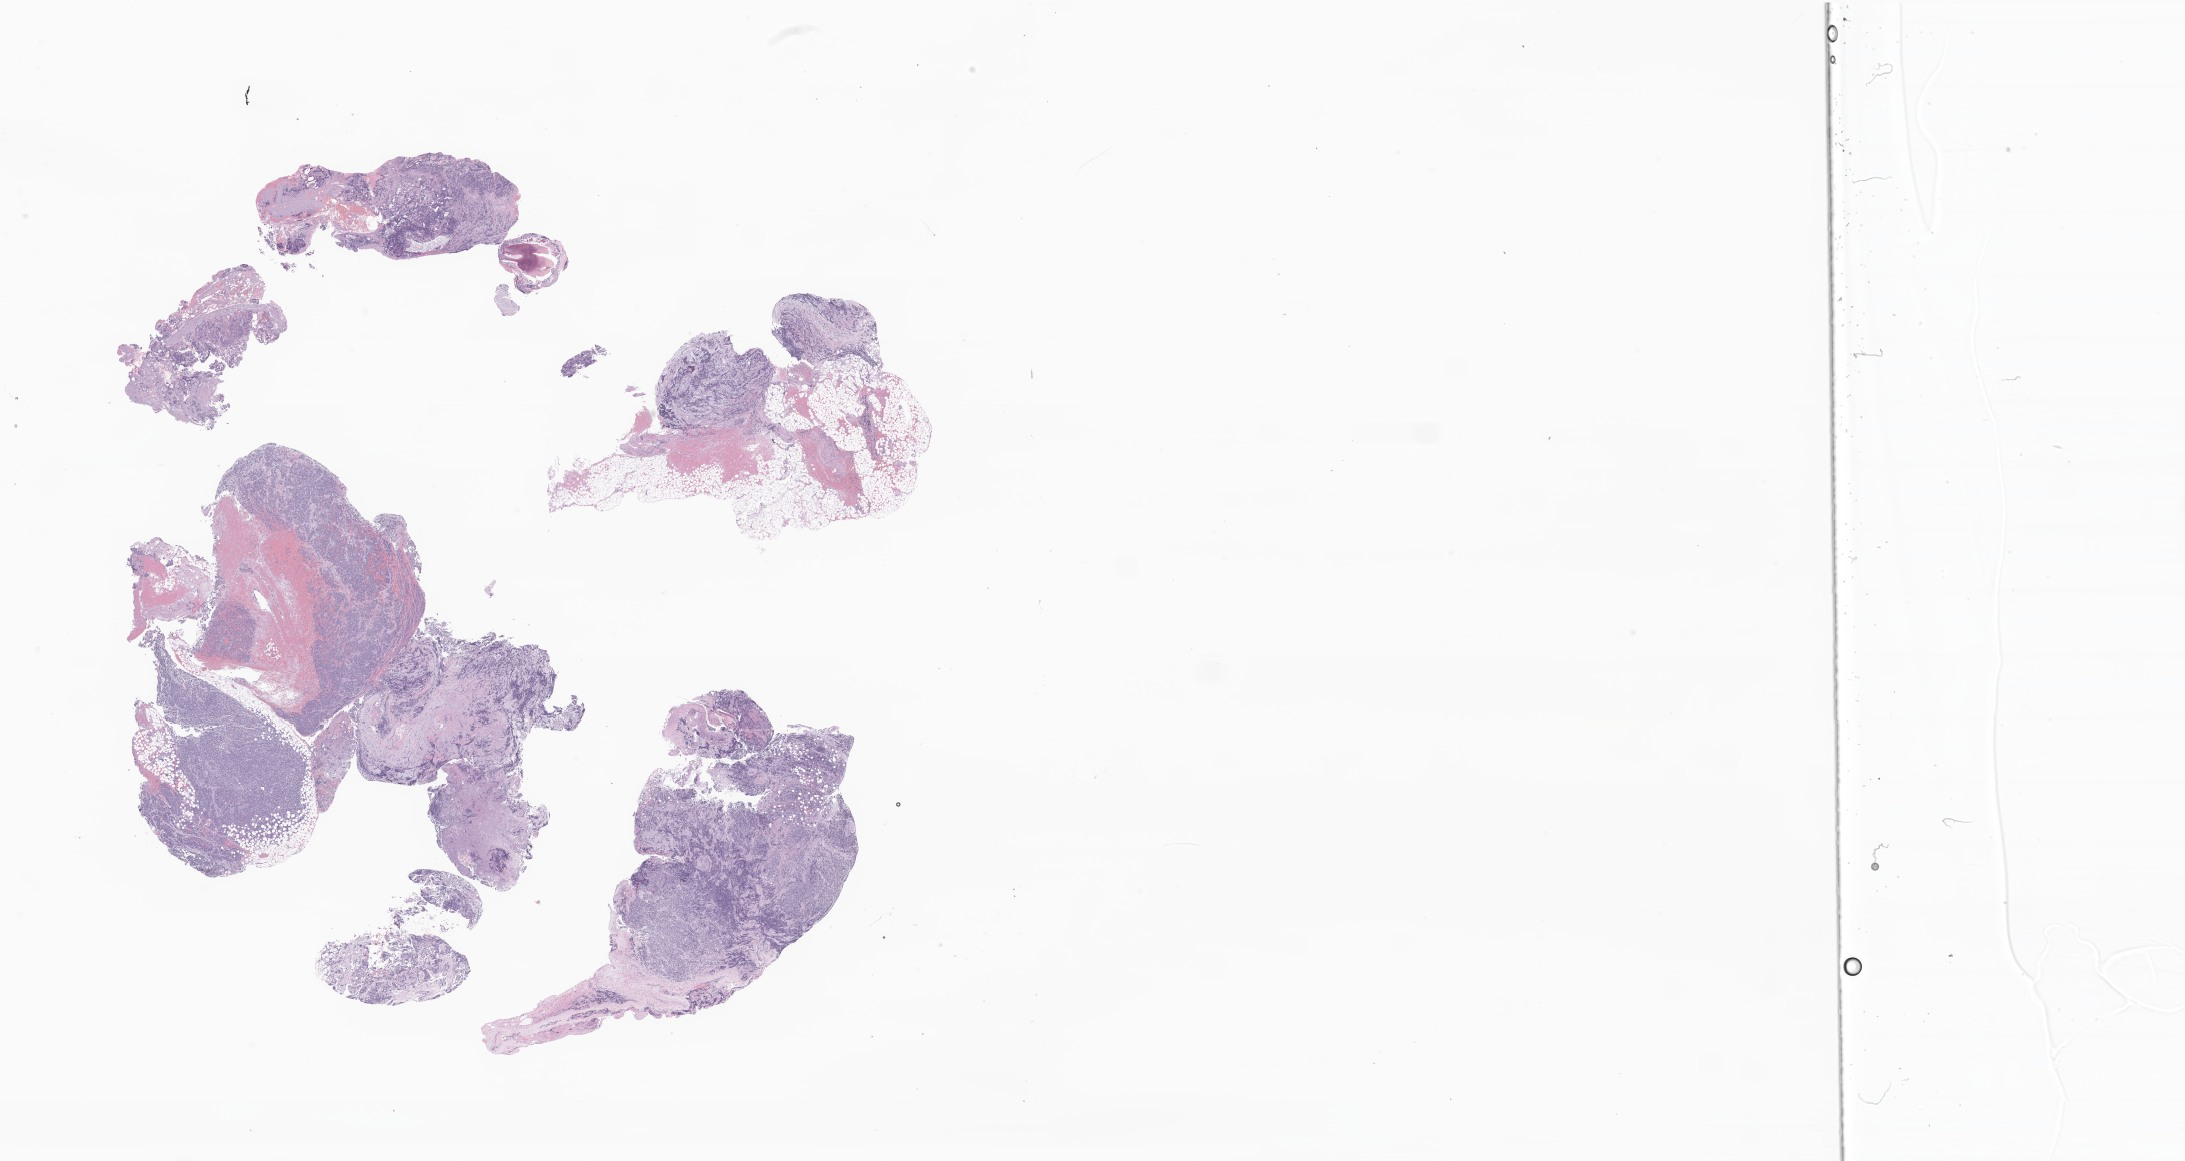
Digitized haematoxylin and eosin-stained section of tumor tissue from the adrenal gland, shown as a low-resolution overview of the whole scanned area (about 36.9 x 19.6 mm), formalin-fixed paraffin-embedded section. Female patient, age 814 days (about 2.2 years).
Diagnosis (ICD-O-3 morphology term): Neuroblastoma, NOS.